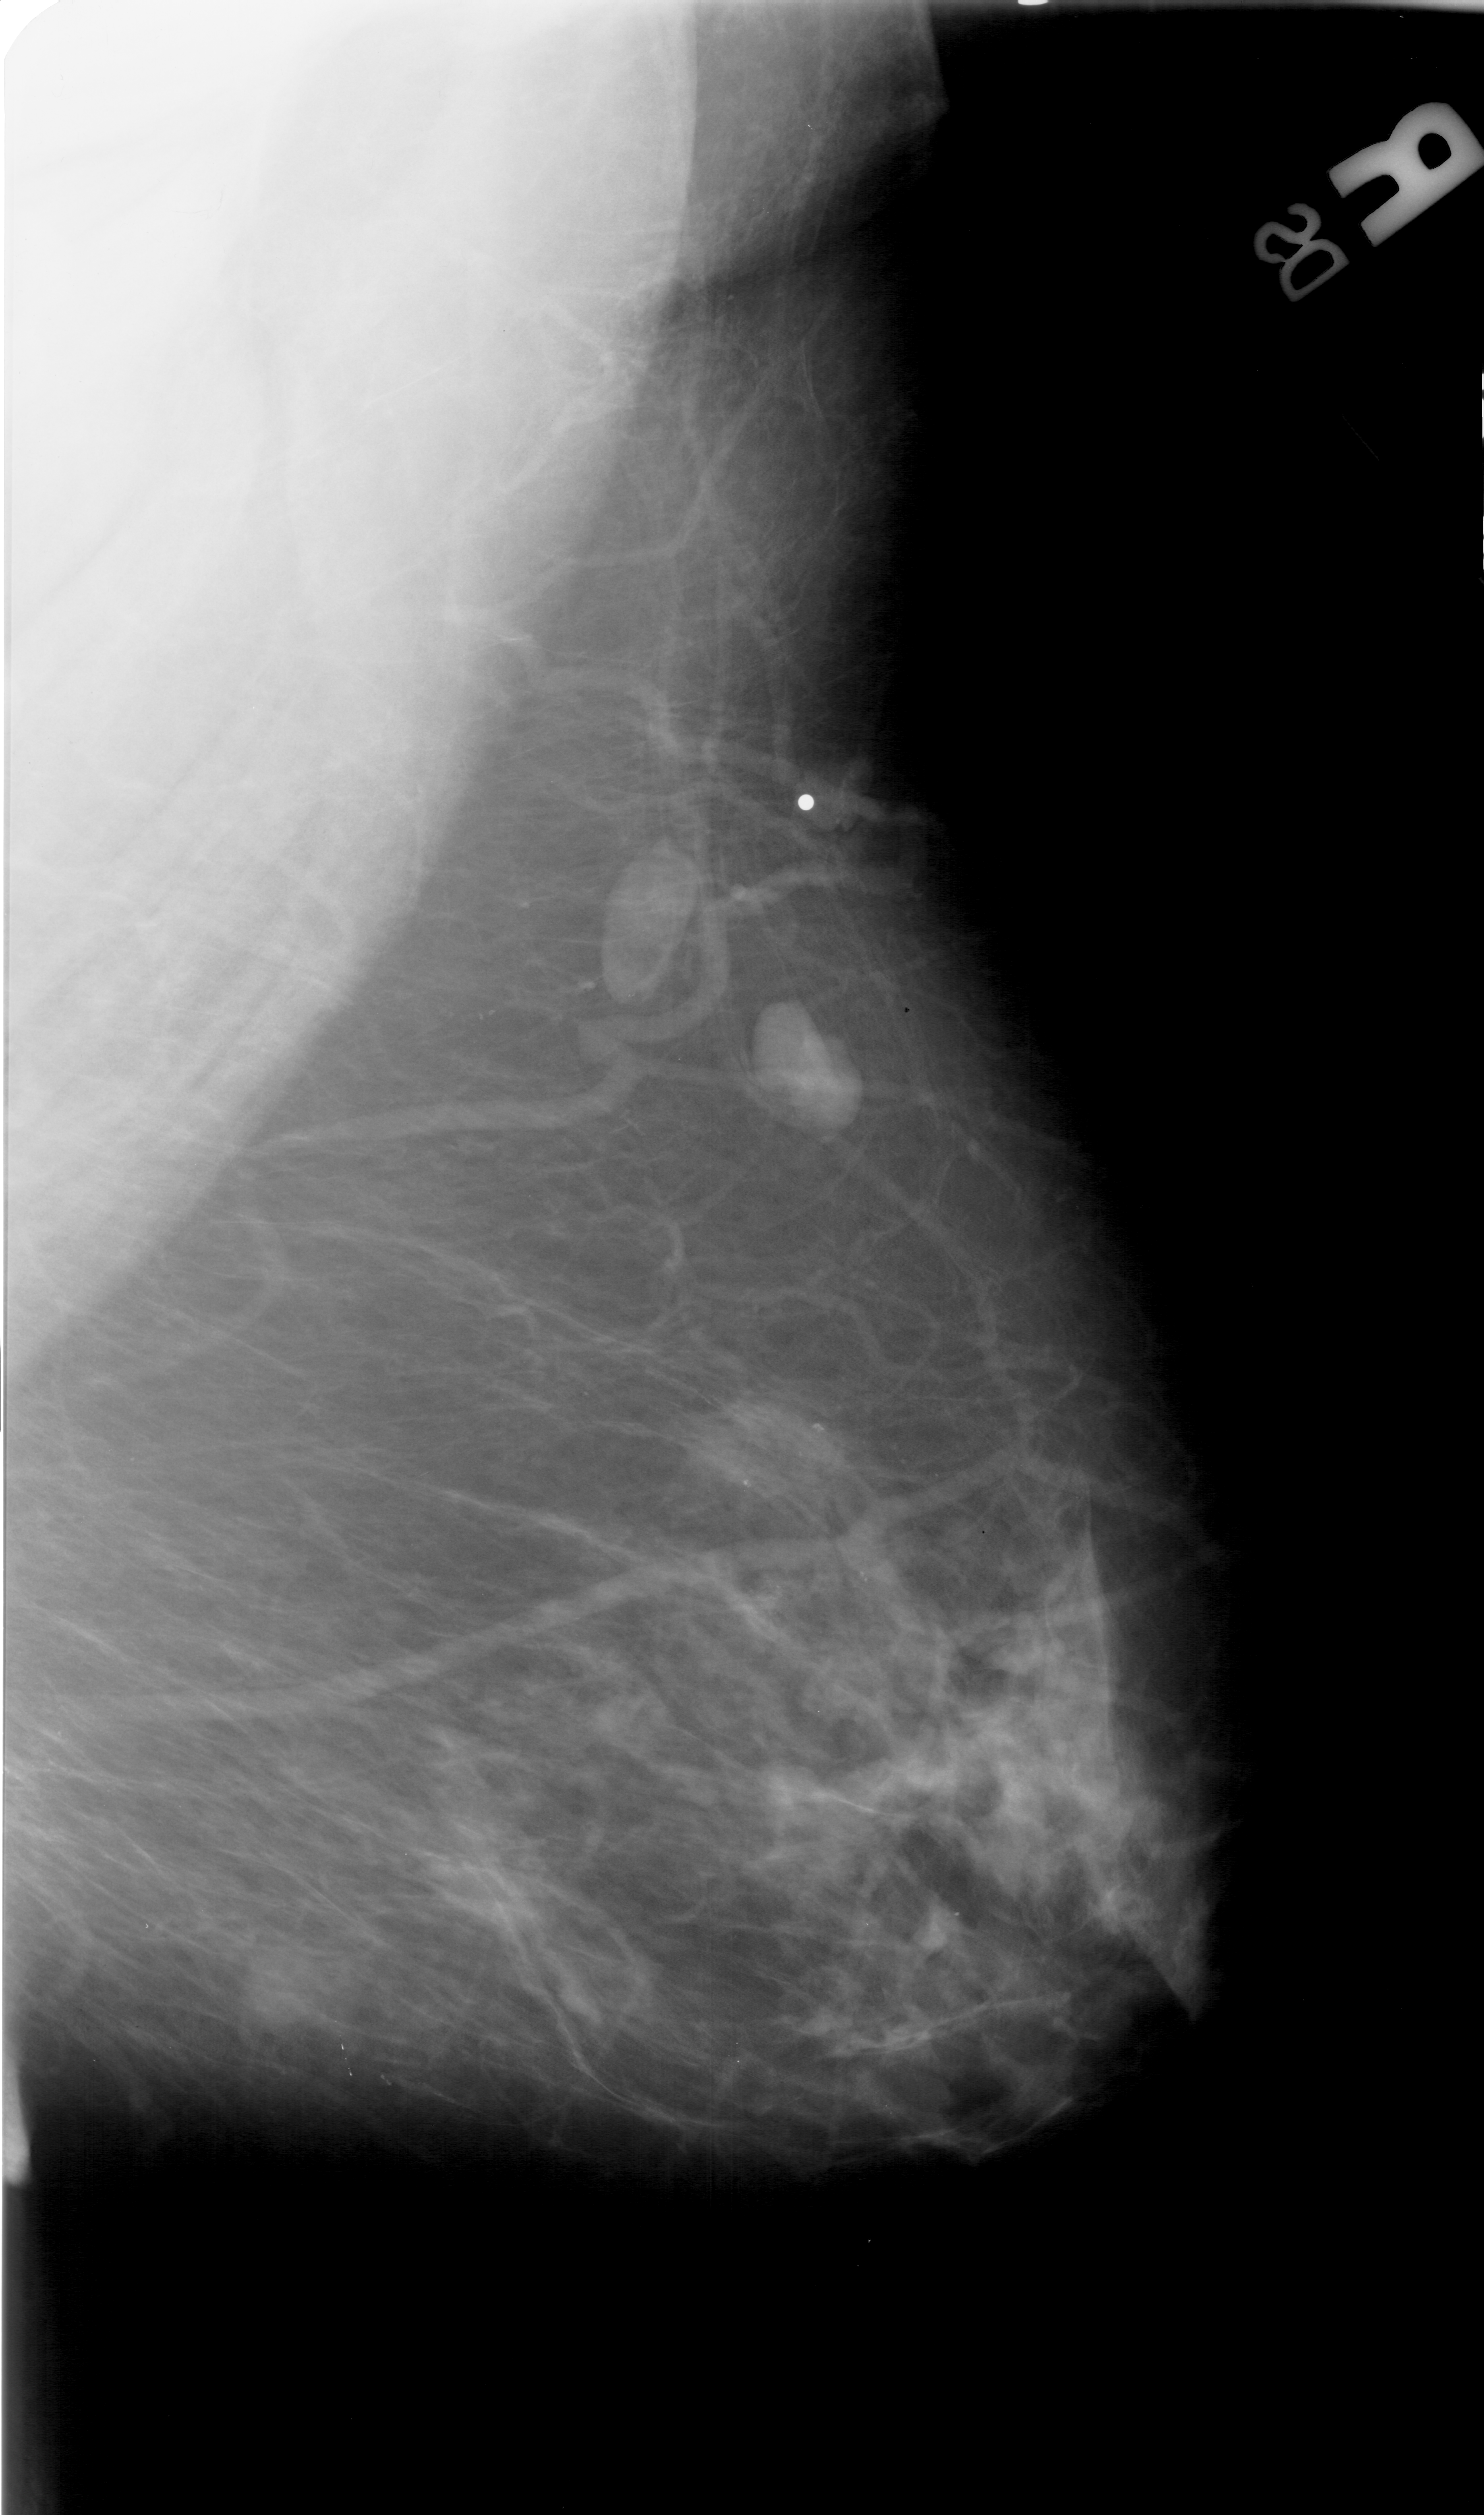
Digitized screen-film mammogram, right breast, mediolateral oblique (MLO) view.
Marked abnormality: calcifications, morphology pleomorphic, distribution clustered; BI-RADS assessment category 3; pathology (as recorded): benign.